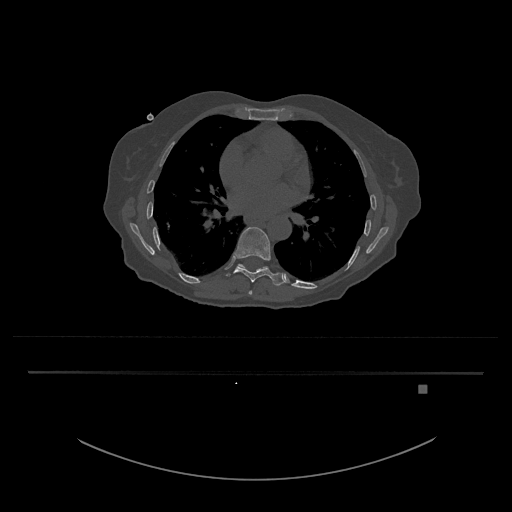
CT including the spine, one axial slice; position 755 of 797 along the scan axis; 120 kVp; bone window (W 1800 / L 400 HU); 0.5 mm slice thickness; 512 × 512 image matrix. Female patient, age 57 years. Case-level facts recorded for this patient, not image findings: primary cancer: cervical.
Outlined on this slice (semi-automatic segmentation, software-assisted and operator-edited):
- T10 vertebra: bounding box [x1, y1, x2, y2] px = [238, 264, 268, 272]
- T8 vertebra: [248, 290, 252, 295]
- T9 vertebra: [227, 227, 284, 286]